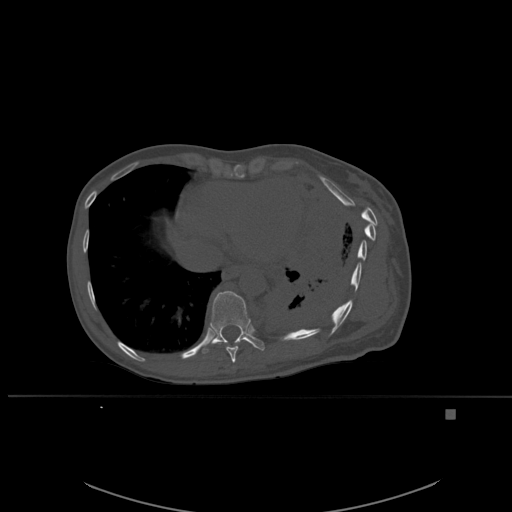
CT including the spine, one axial slice. Position 324 of 537 along the scan axis. Bone window (W 1800 / L 400 HU). 1.5 mm slice thickness. 512 × 512 image matrix, field of view 440 × 440 mm. Patient: female, 45 years. Case-level facts recorded for this patient, not image findings: primary cancer: lung.
Structures marked on this image (semi-automatic segmentation, software-assisted and operator-edited):
- T10 vertebra: box from (x=202, y=291) to (x=265, y=354) px
- T9 vertebra: (x=222, y=341)–(x=241, y=363)